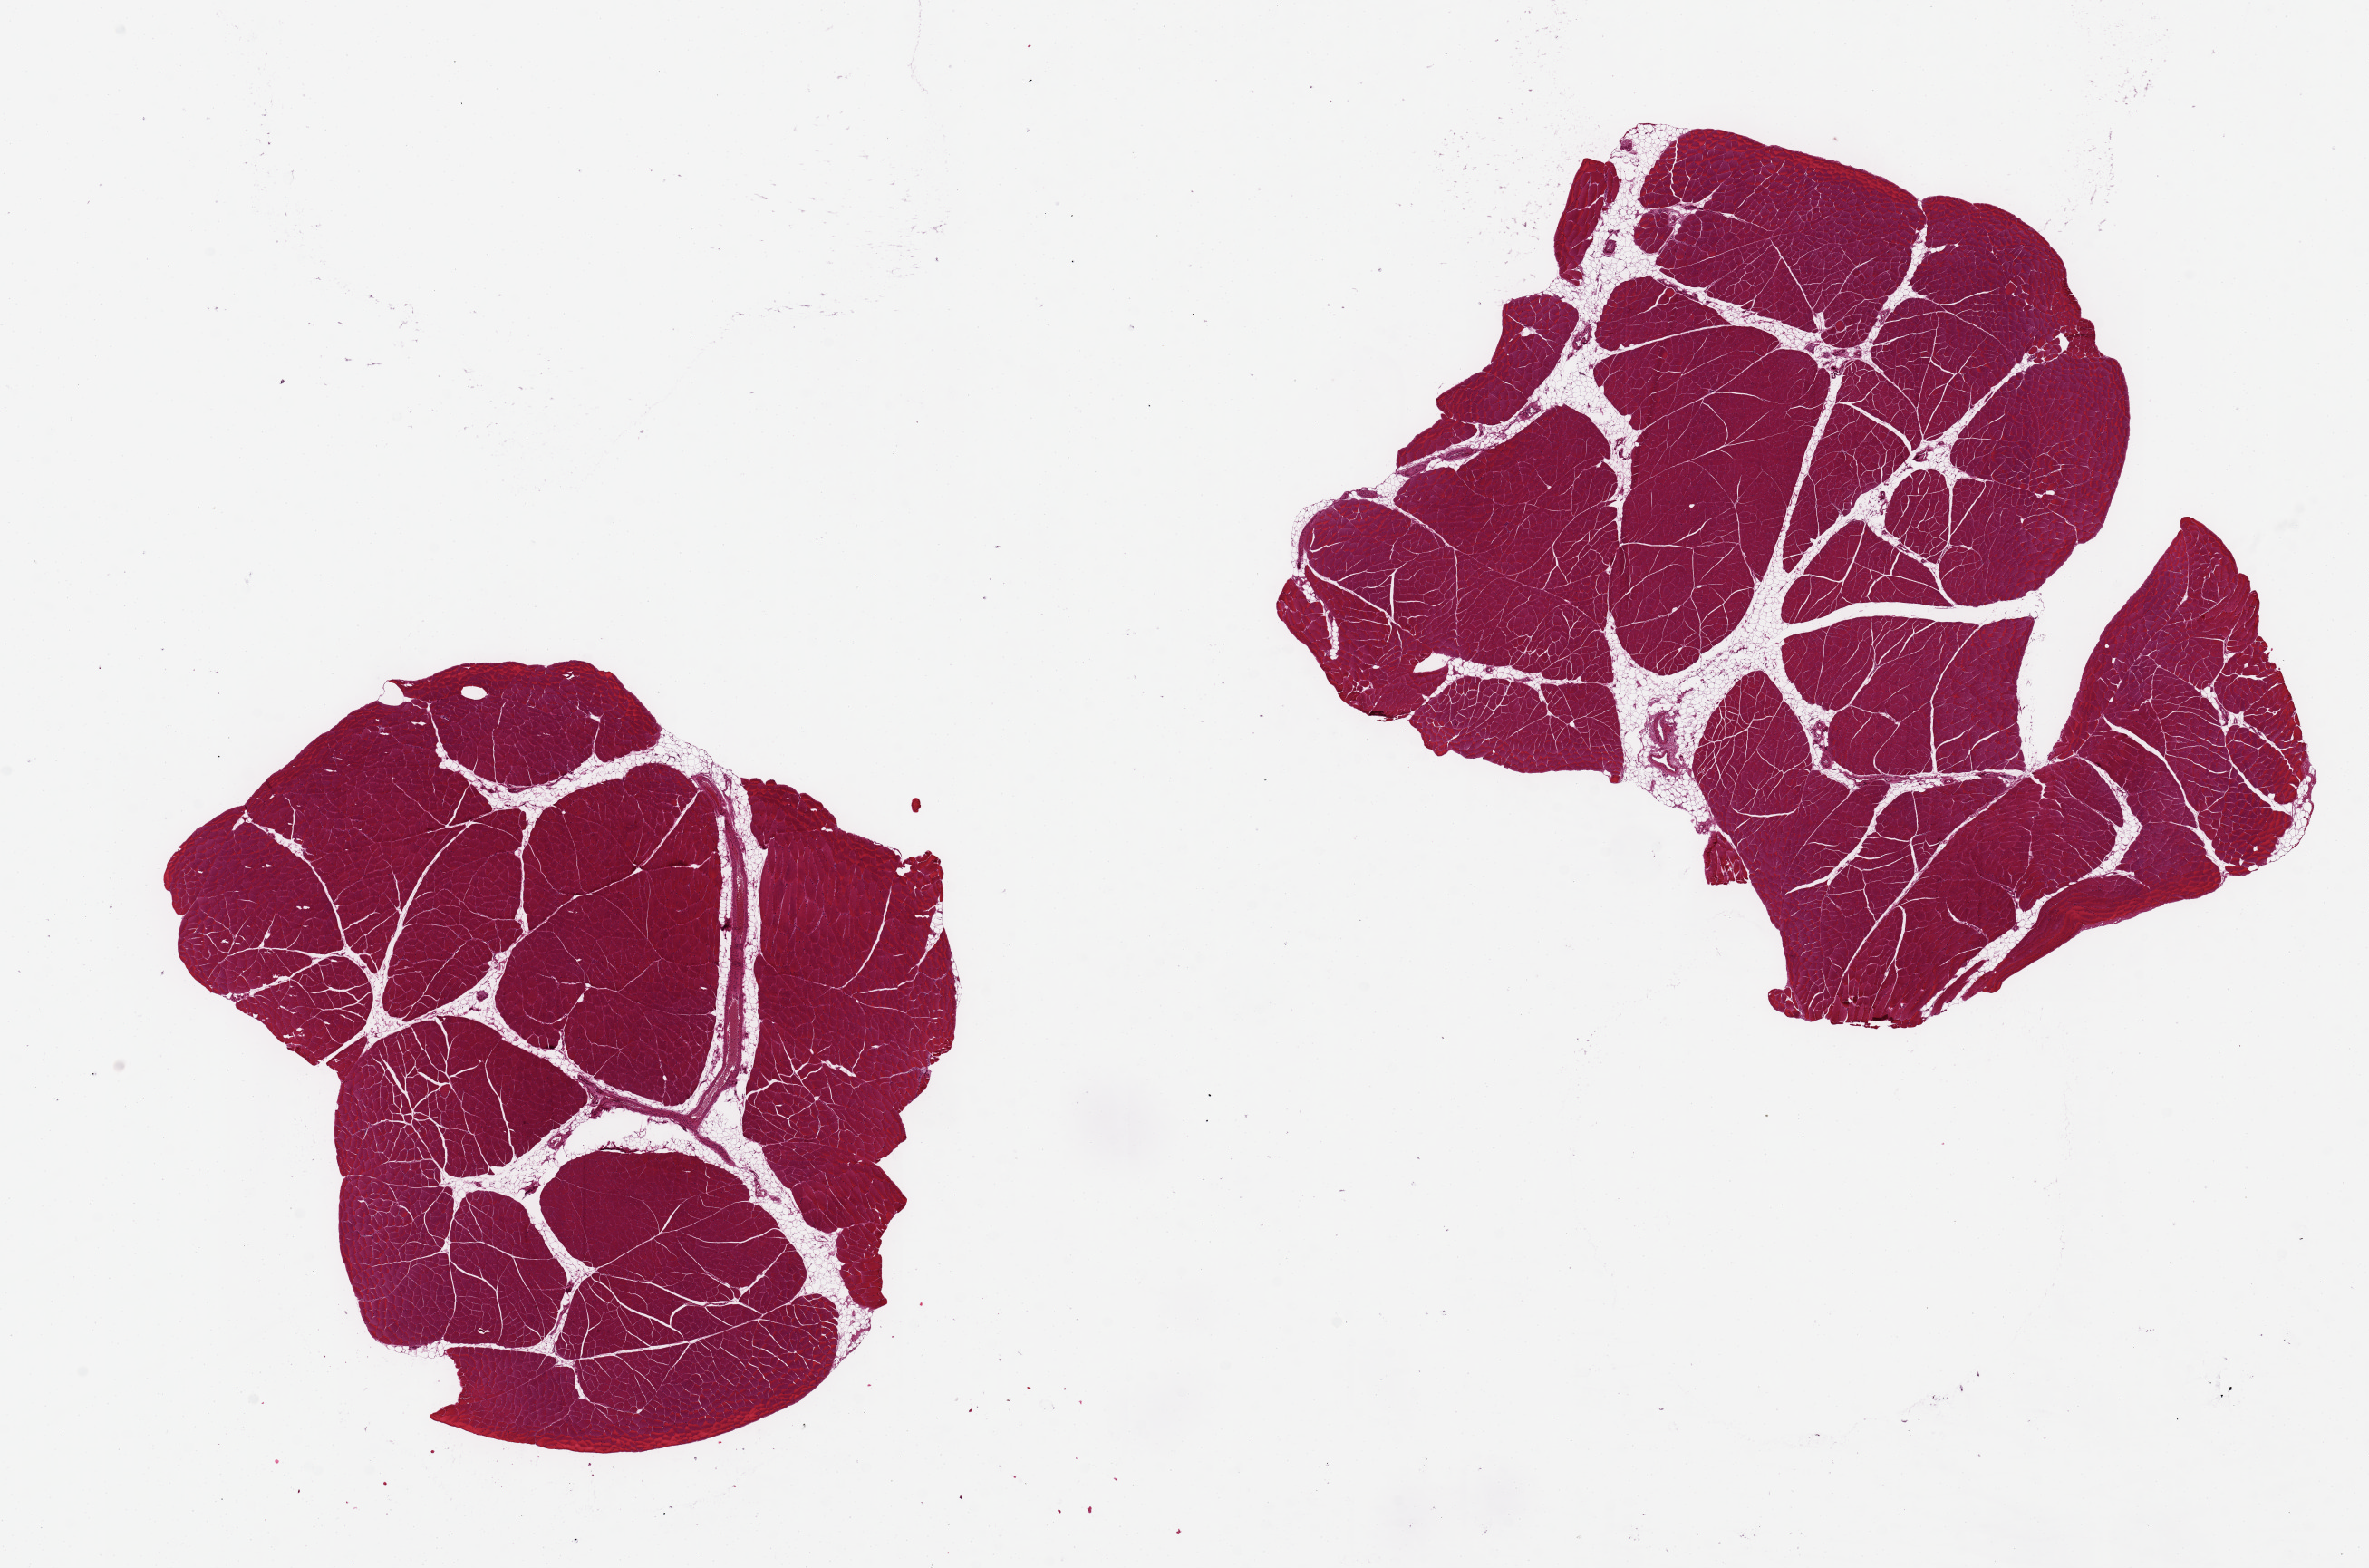
Whole-slide image, haematoxylin and eosin stain, brightfield, whole scanned area (about 20.7 x 13.7 mm) shown as a low-resolution overview. PAXgene-fixed, paraffin-embedded tissue. Section of skeletal muscle (target tissue). Tissue donor sample. Donor sex: male.
Review note (as recorded): 2 pieces, ~8x6mm, minimal interstitial fat.